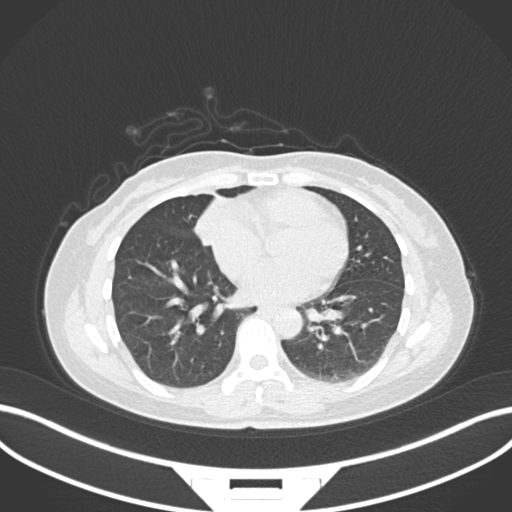
Chest CT, one axial slice; slice 62 of 171 in the series (ordered by position); reconstruction kernel B30f; lung window (W 1500 / L -600 HU); 1 mm slice thickness; 512 × 512 image matrix, field of view 400 × 400 mm. Patient: female, 43 years. From the clinical record (not read from this slice): clinical TNM (as recorded): T1c N3 M1; histopathological grade: G1.
Structures marked on this image (rectangle marked by the reading radiologist):
- lung tumour (recorded histology: adenocarcinoma): bounding box <192,194,218,248> (left, top, right, bottom; pixels)